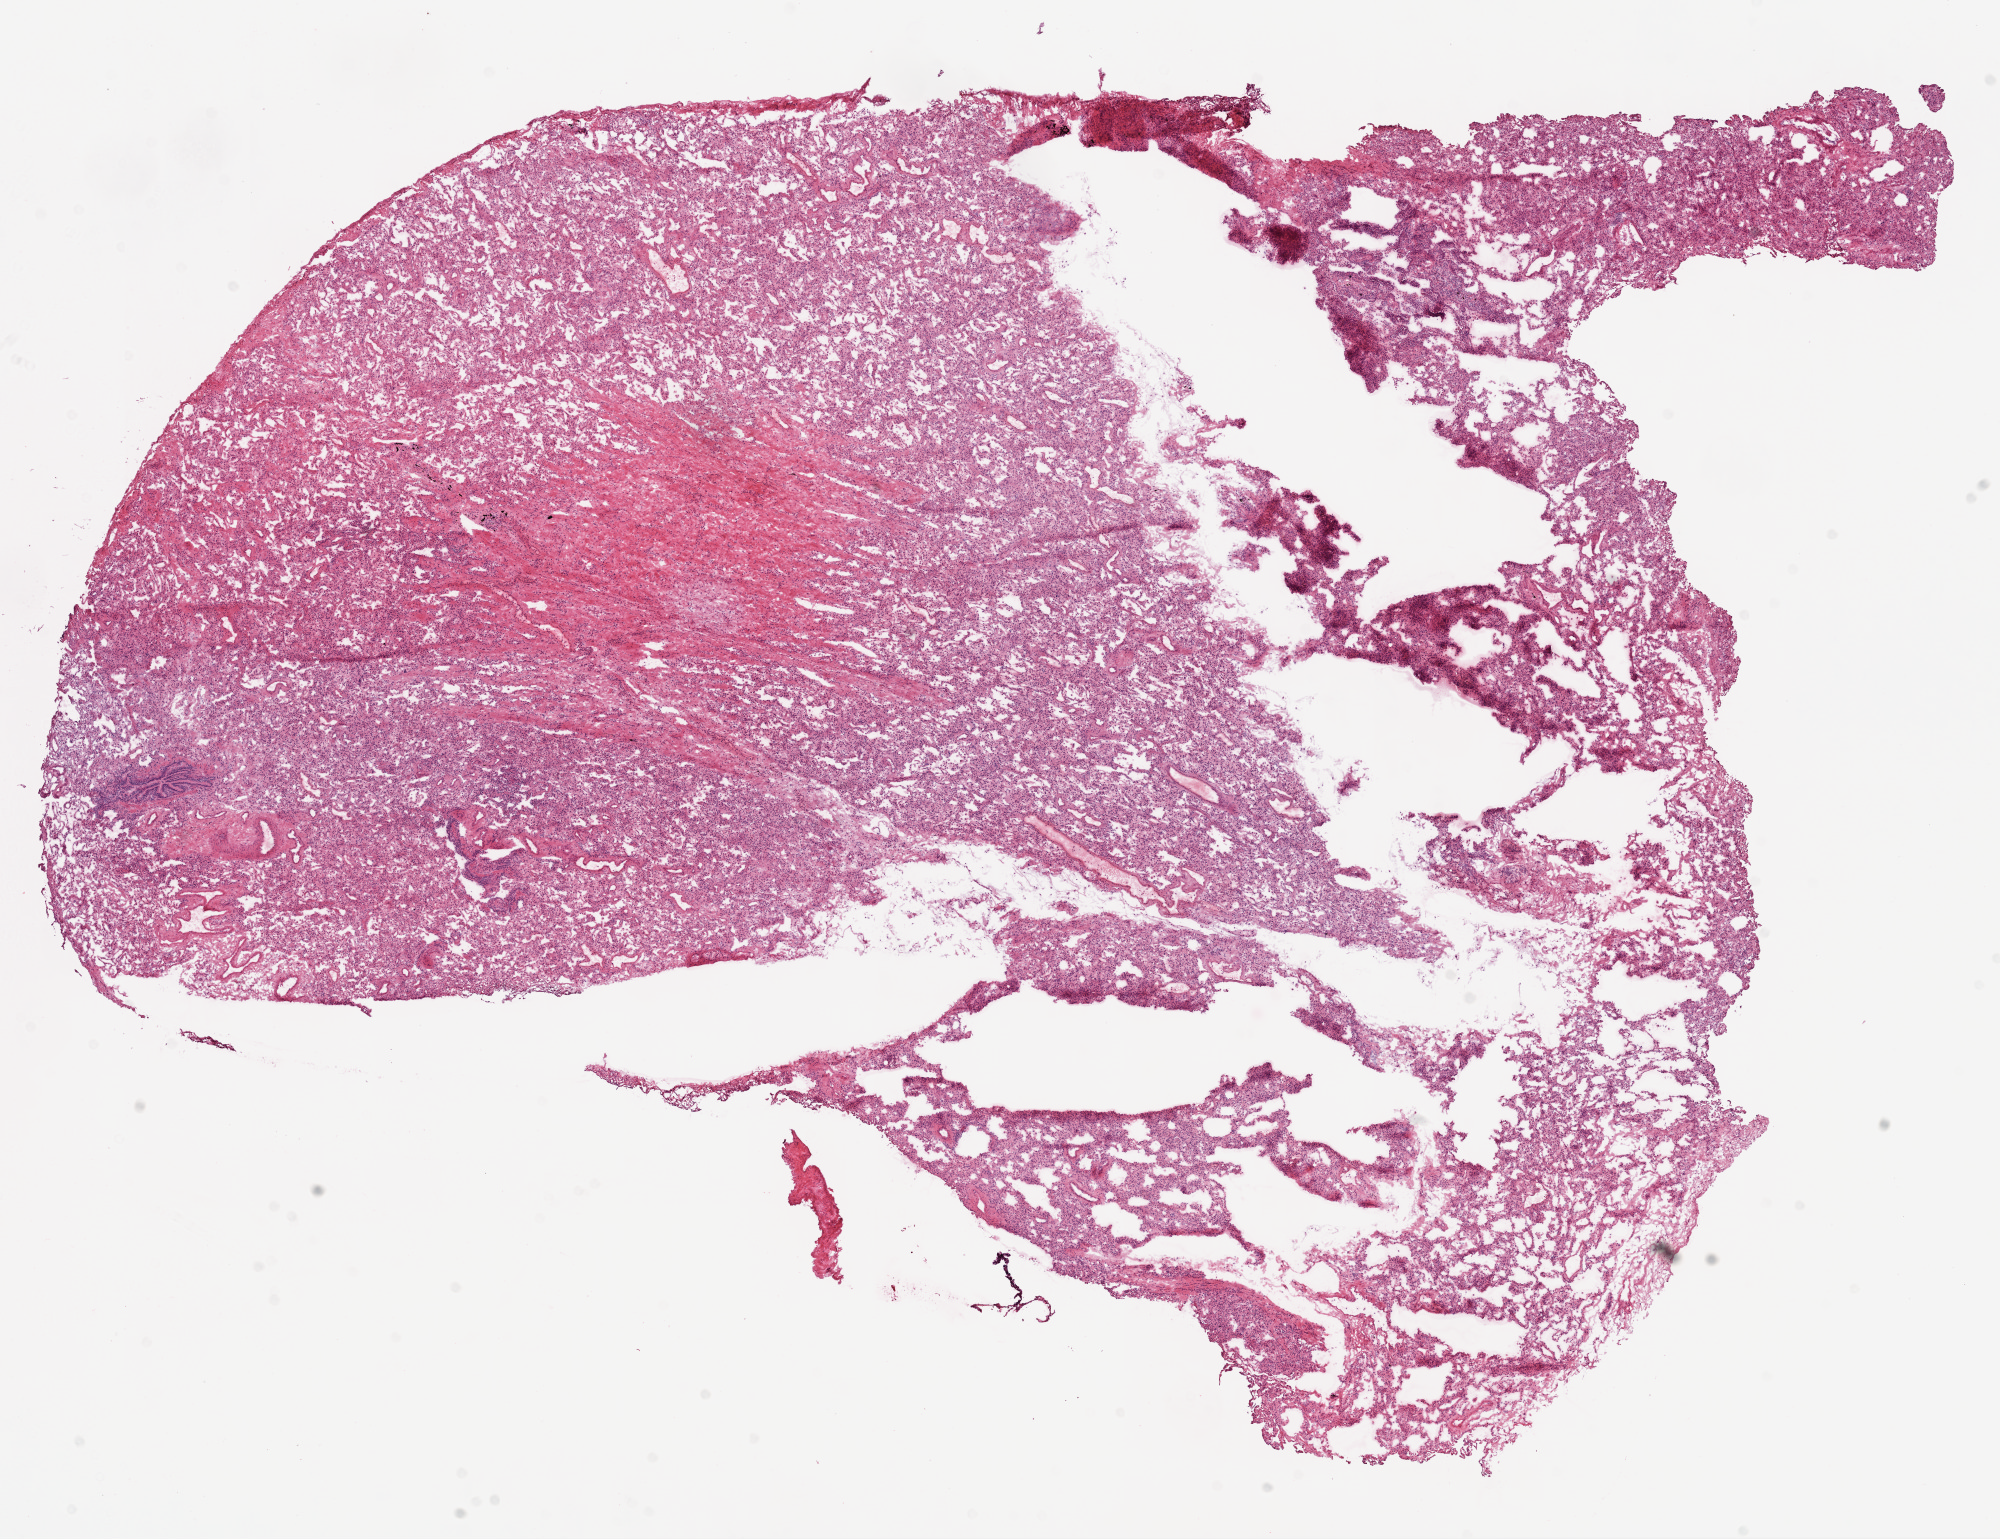
Digitized Hematoxylin and eosin (H&E) stained tissue section (whole slide) — whole scanned area (about 16.0 x 12.3 mm, acquisition: 20x scan) shown as a low-resolution overview, frozen section, lung, solid tissue normal (non-tumour tissue) sample. Female, age 51 years at initial diagnosis.
* this section: solid tissue normal sample (biorepository sample class)
* patient diagnosis: Adenocarcinoma, NOS